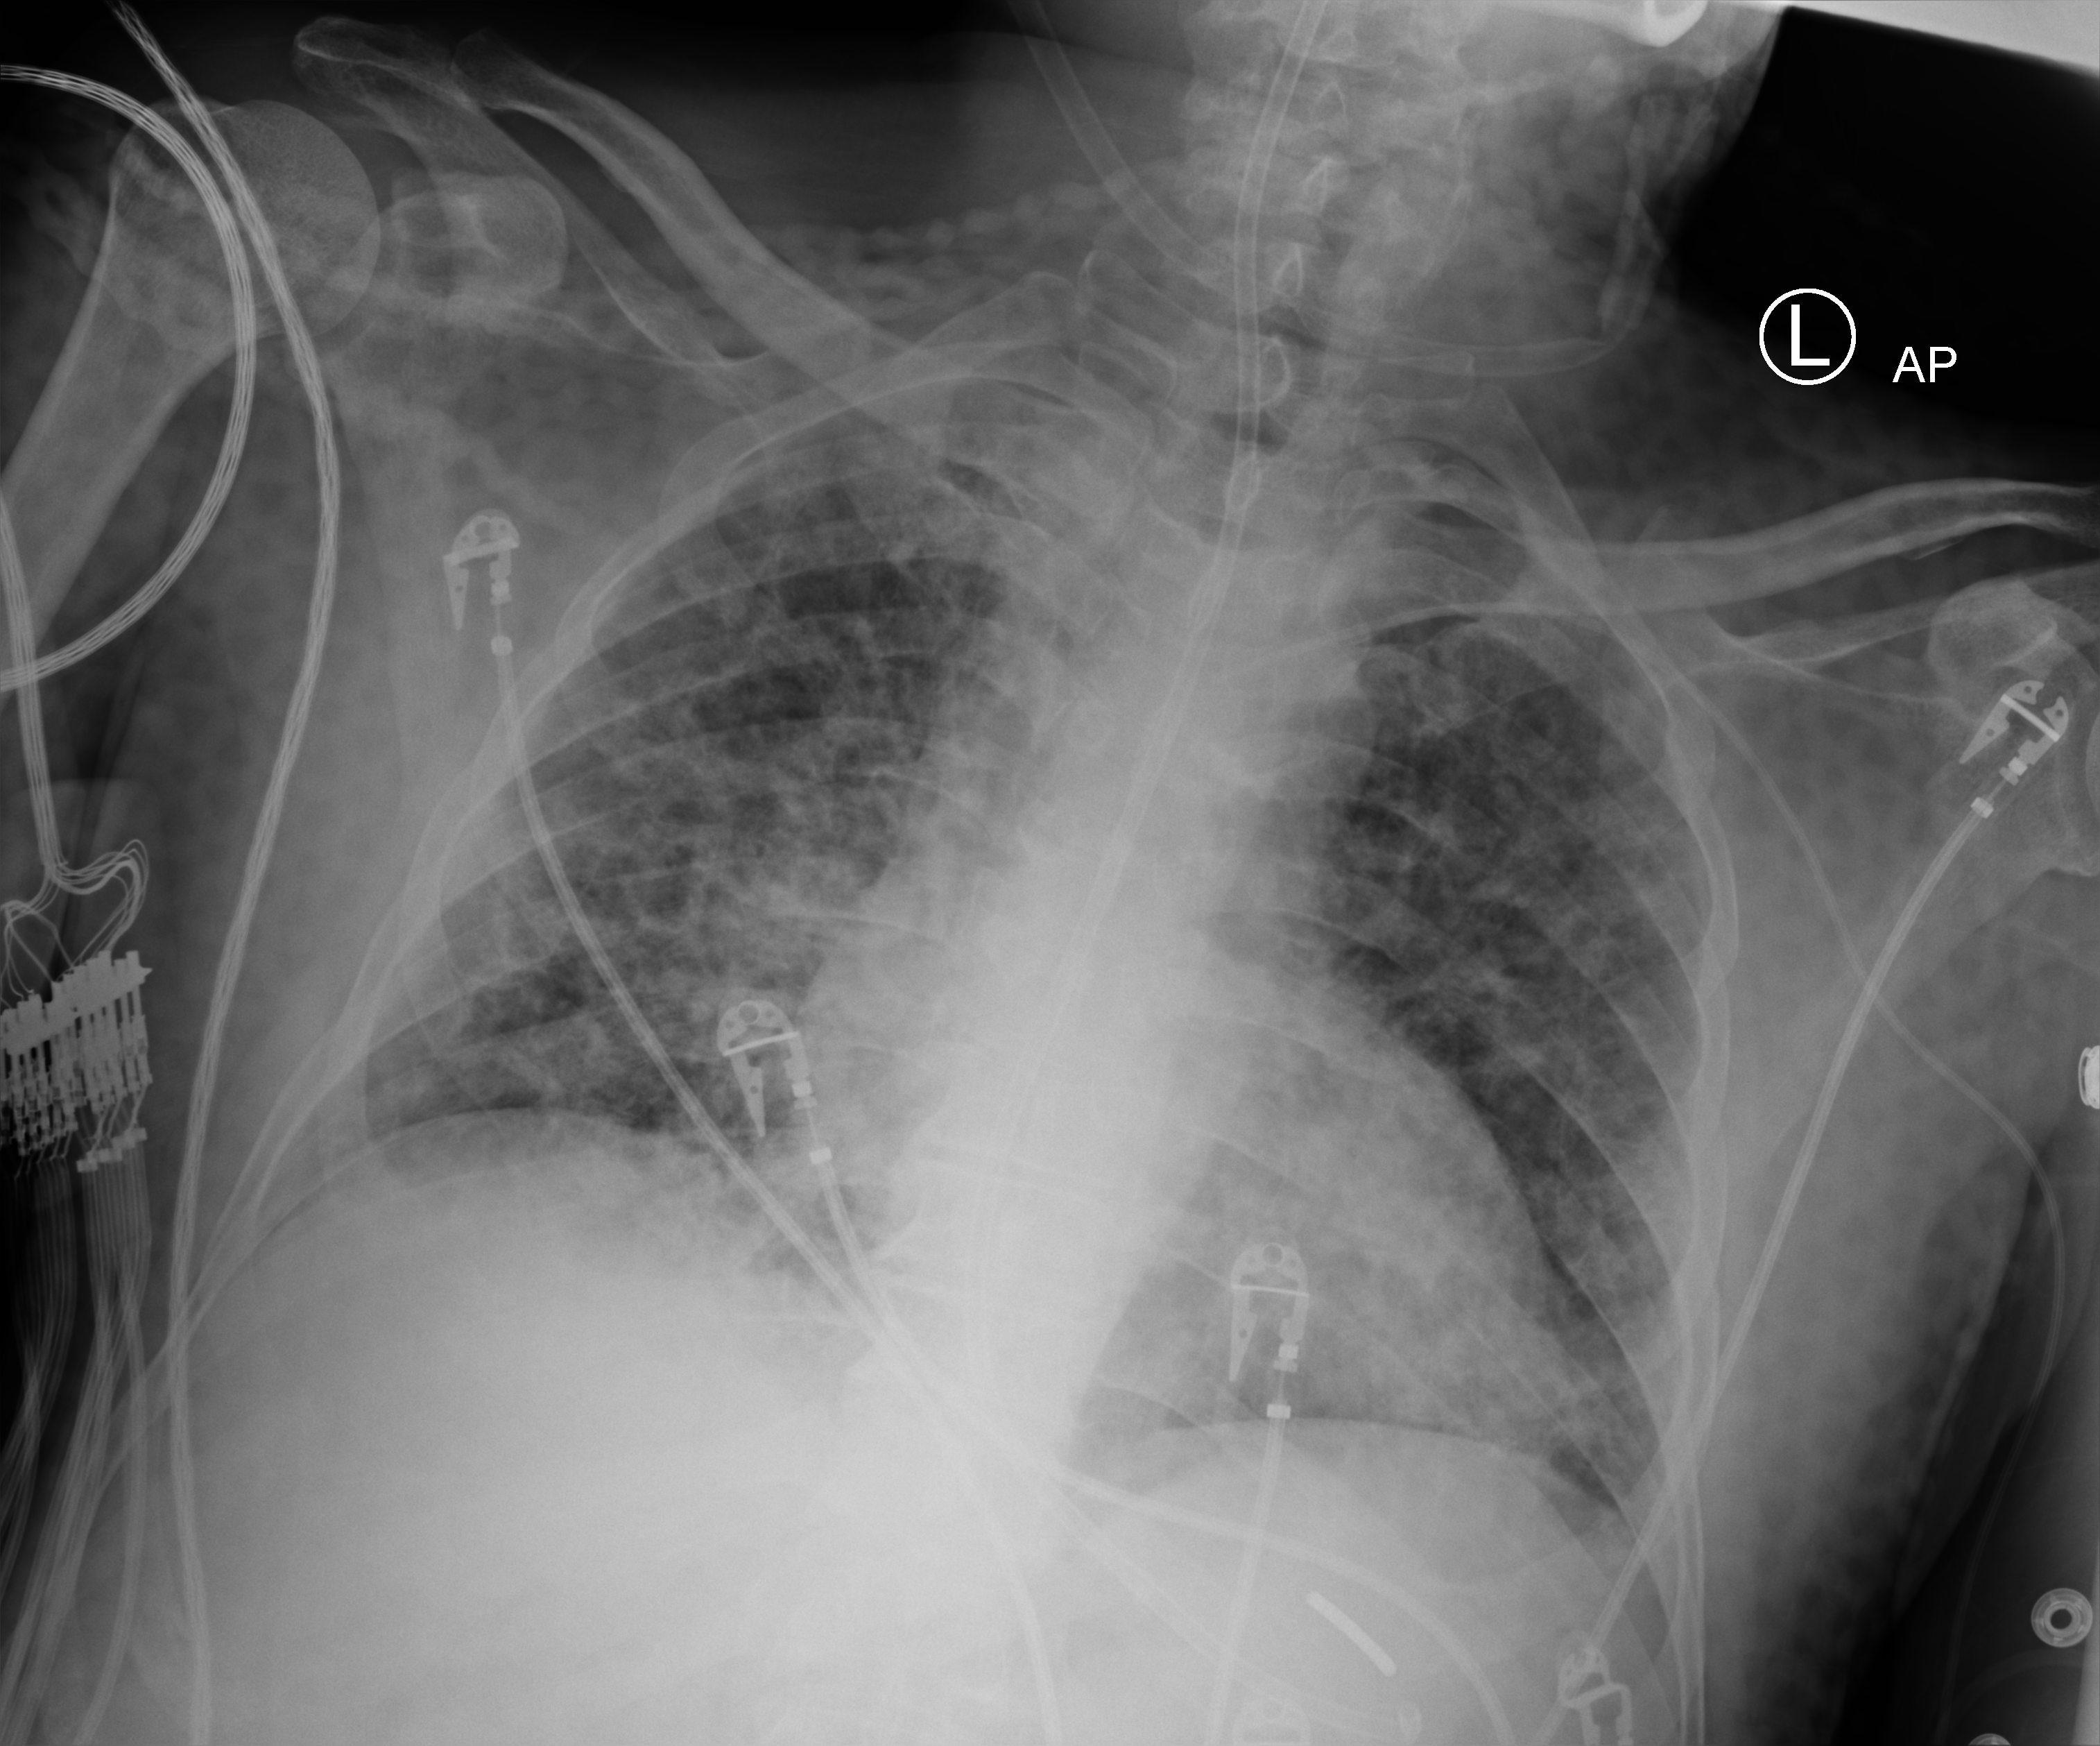
Bedside chest radiograph (computed radiography); anteroposterior (AP) projection. Male patient hospitalised with COVID-19, age 18–59 years.
Admission-level facts for this patient (not findings on this image; timing relative to this image not recorded):
- admitted to intensive care during this hospital stay: yes
- chronic kidney disease (admission record): no